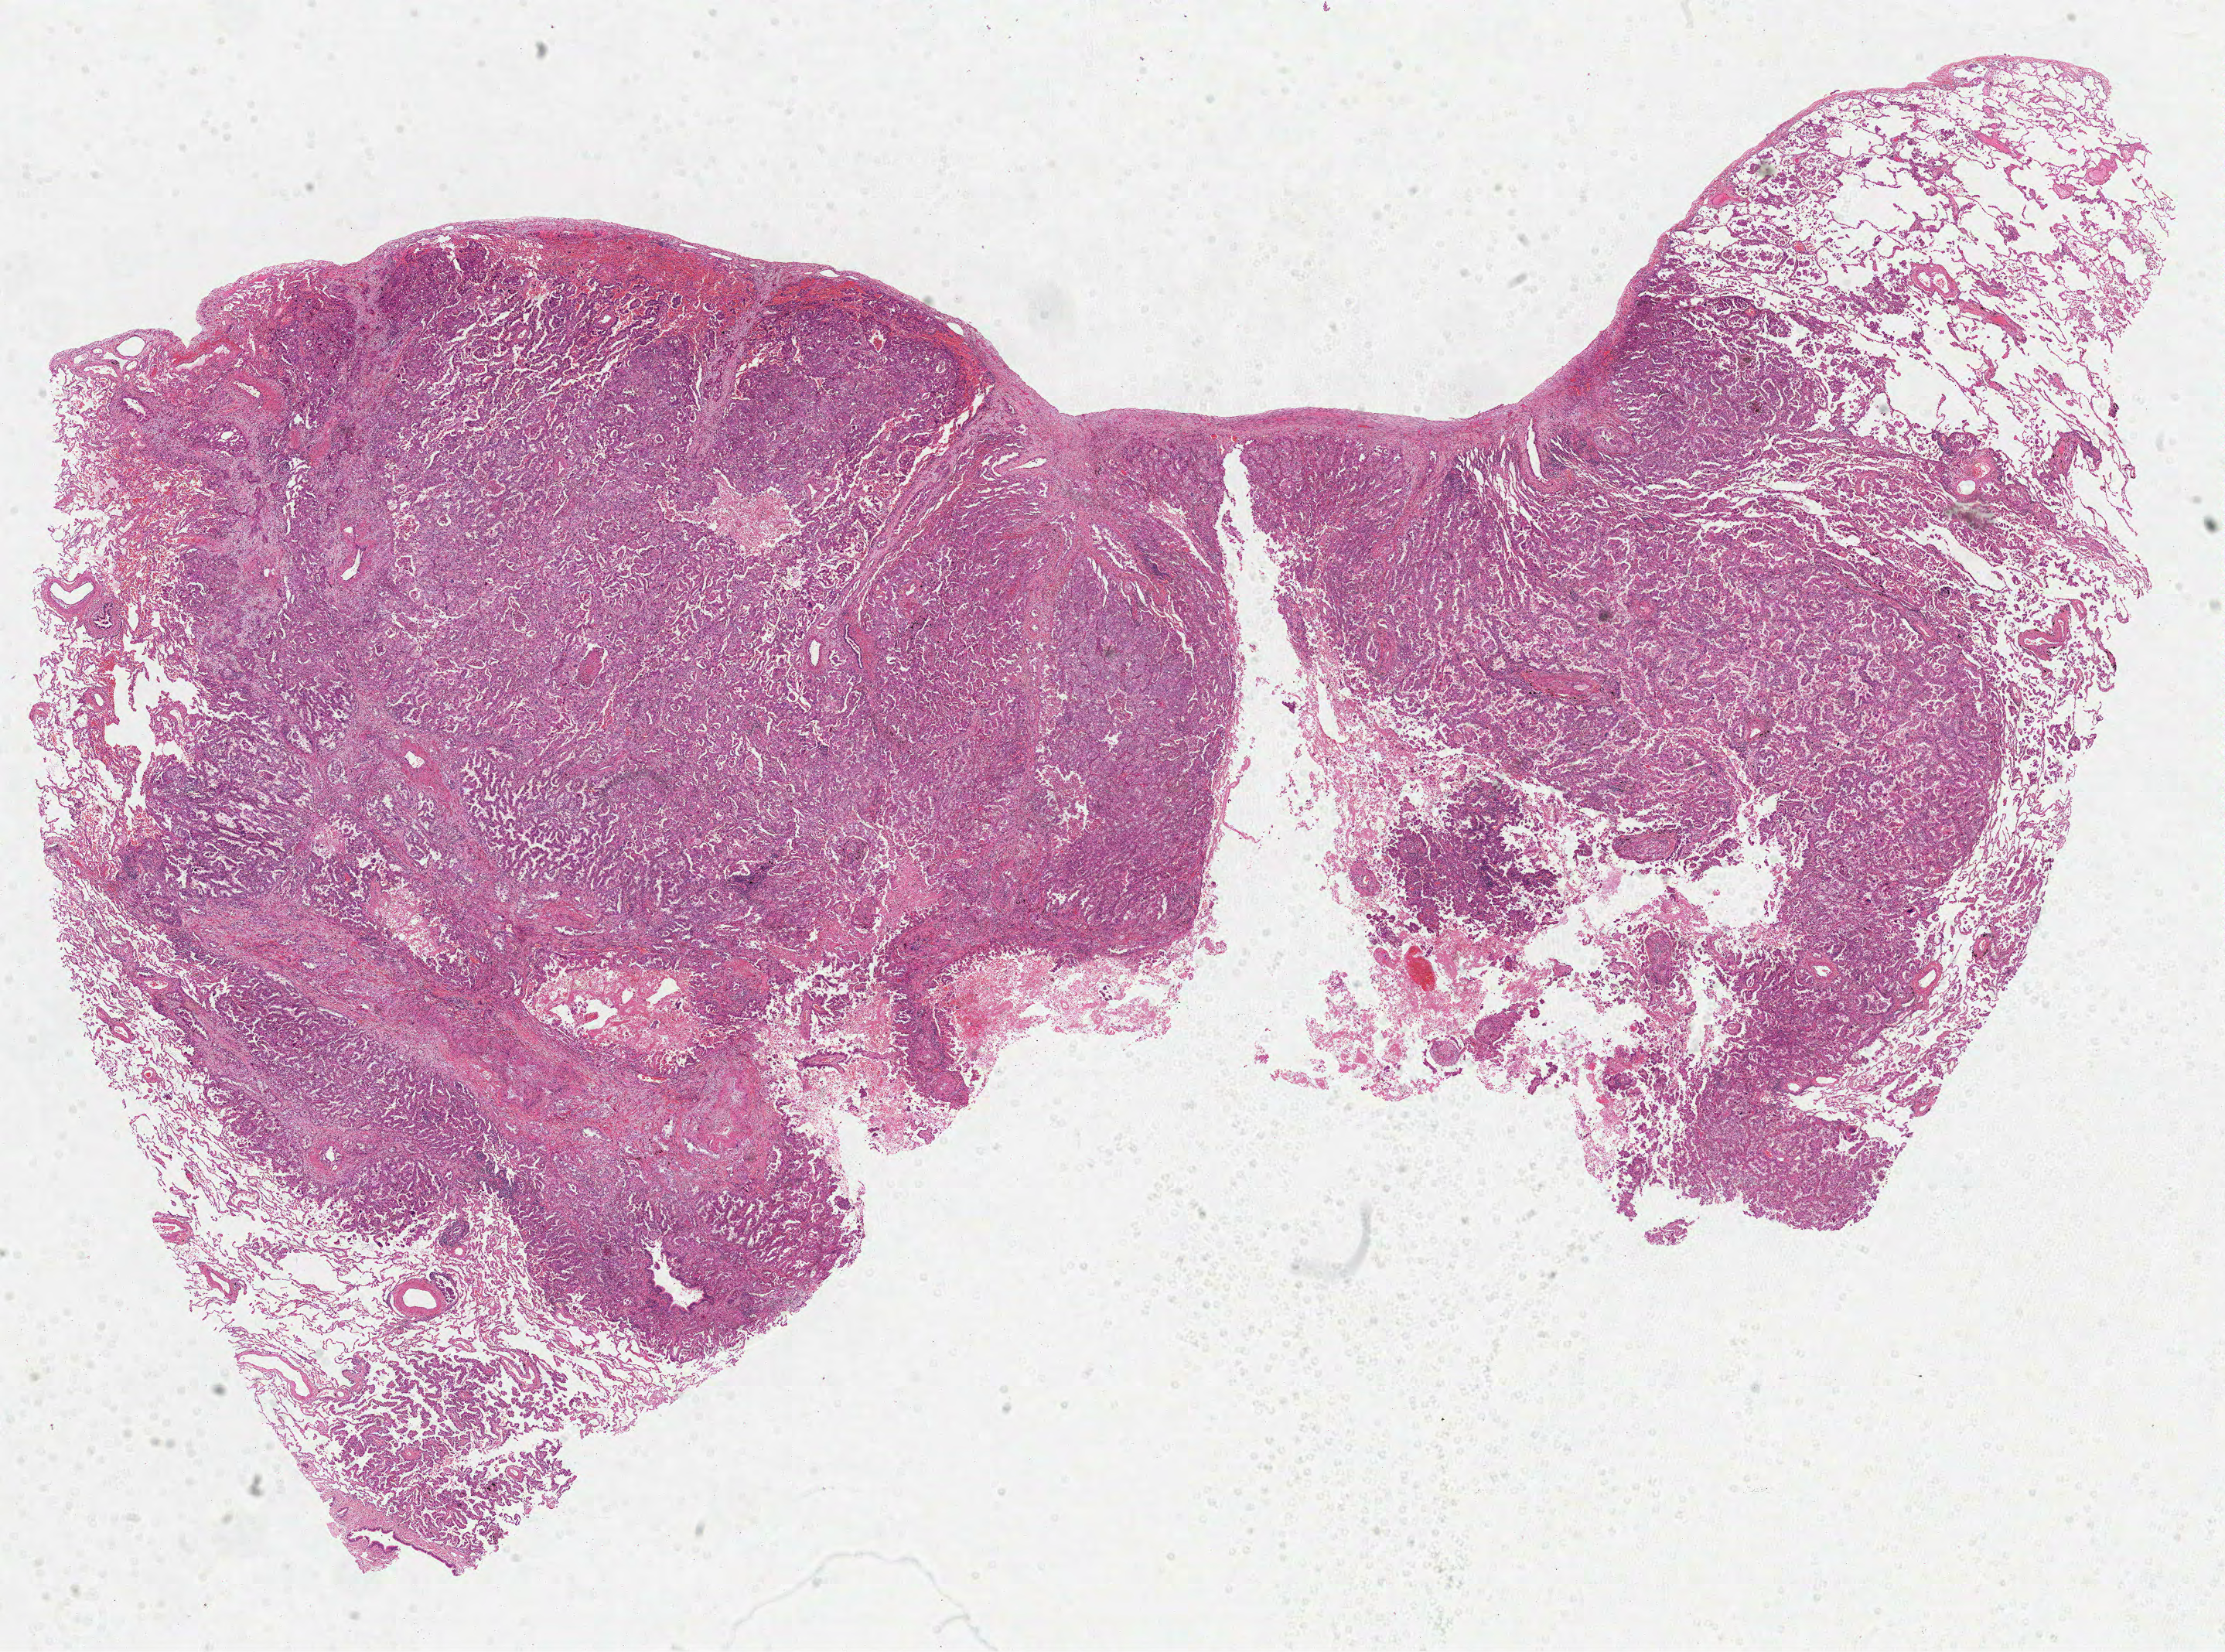
H&E whole-slide image, low-resolution overview of the scanned area, about 23.2 x 17.2 mm; formalin-fixed paraffin-embedded (FFPE) diagnostic section; lung, primary tumour sample. Female patient; age at initial diagnosis 52 years.
AJCC pathologic stage: IV (6th edition). Laterality: right. Diagnosis: Adenocarcinoma, NOS (middle lobe, lung). TNM: T4 N1 M1.